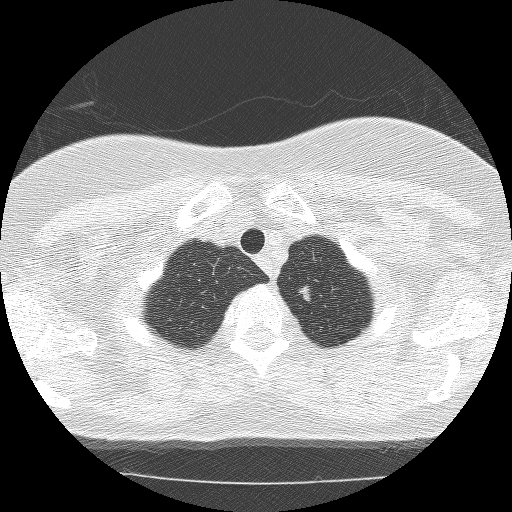
Low-dose screening chest CT, axial slice. Second annual screen. Lung window (W 1500 / L -600 HU). Lung (sharp) reconstruction kernel (BONE). Female, age 59 years at enrolment.
• Lesion marked by an expert reader, bounding box (x1, y1, x2, y2) in pixels: (279, 276, 324, 315).
• The screening reader recorded 3 non-calcified nodules or masses ≥4 mm on this exam; which of them this box marks is not recorded.